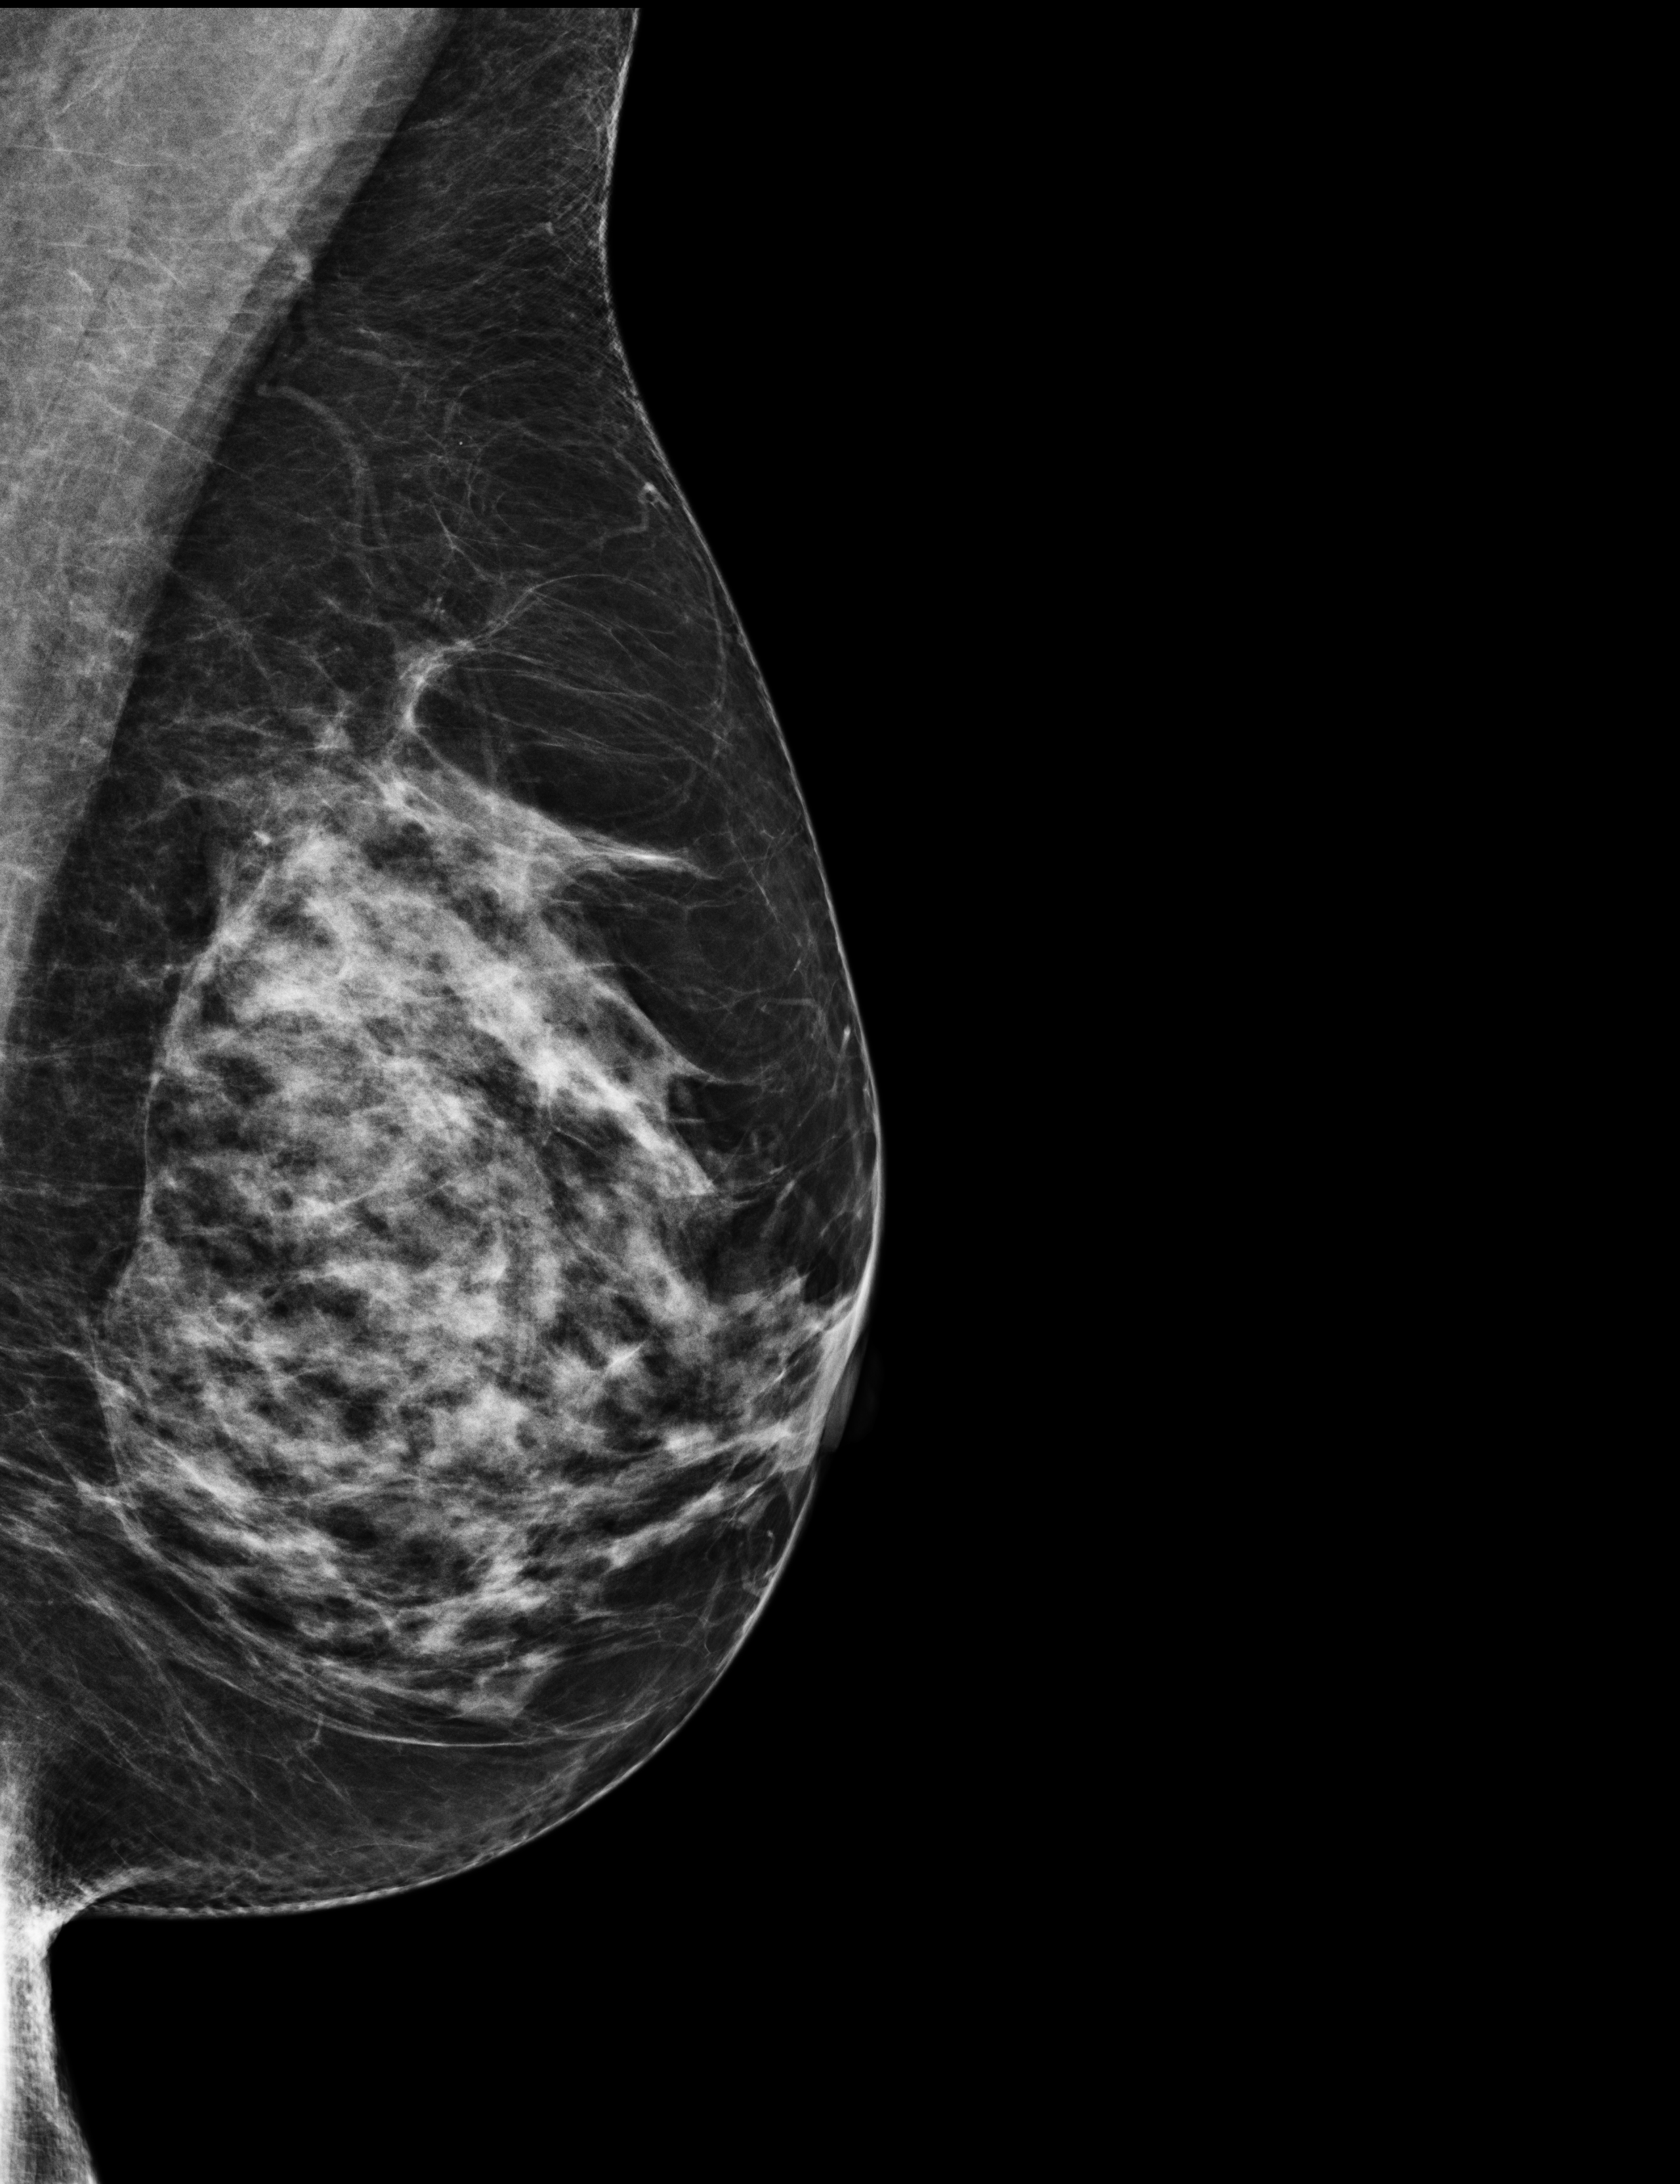
Annual screening mammography examination, compressed breast thickness 59 mm. Female patient, age 59 years.
Image type: full-field digital mammogram. Breast: left. Projection: medio-lateral oblique projection.